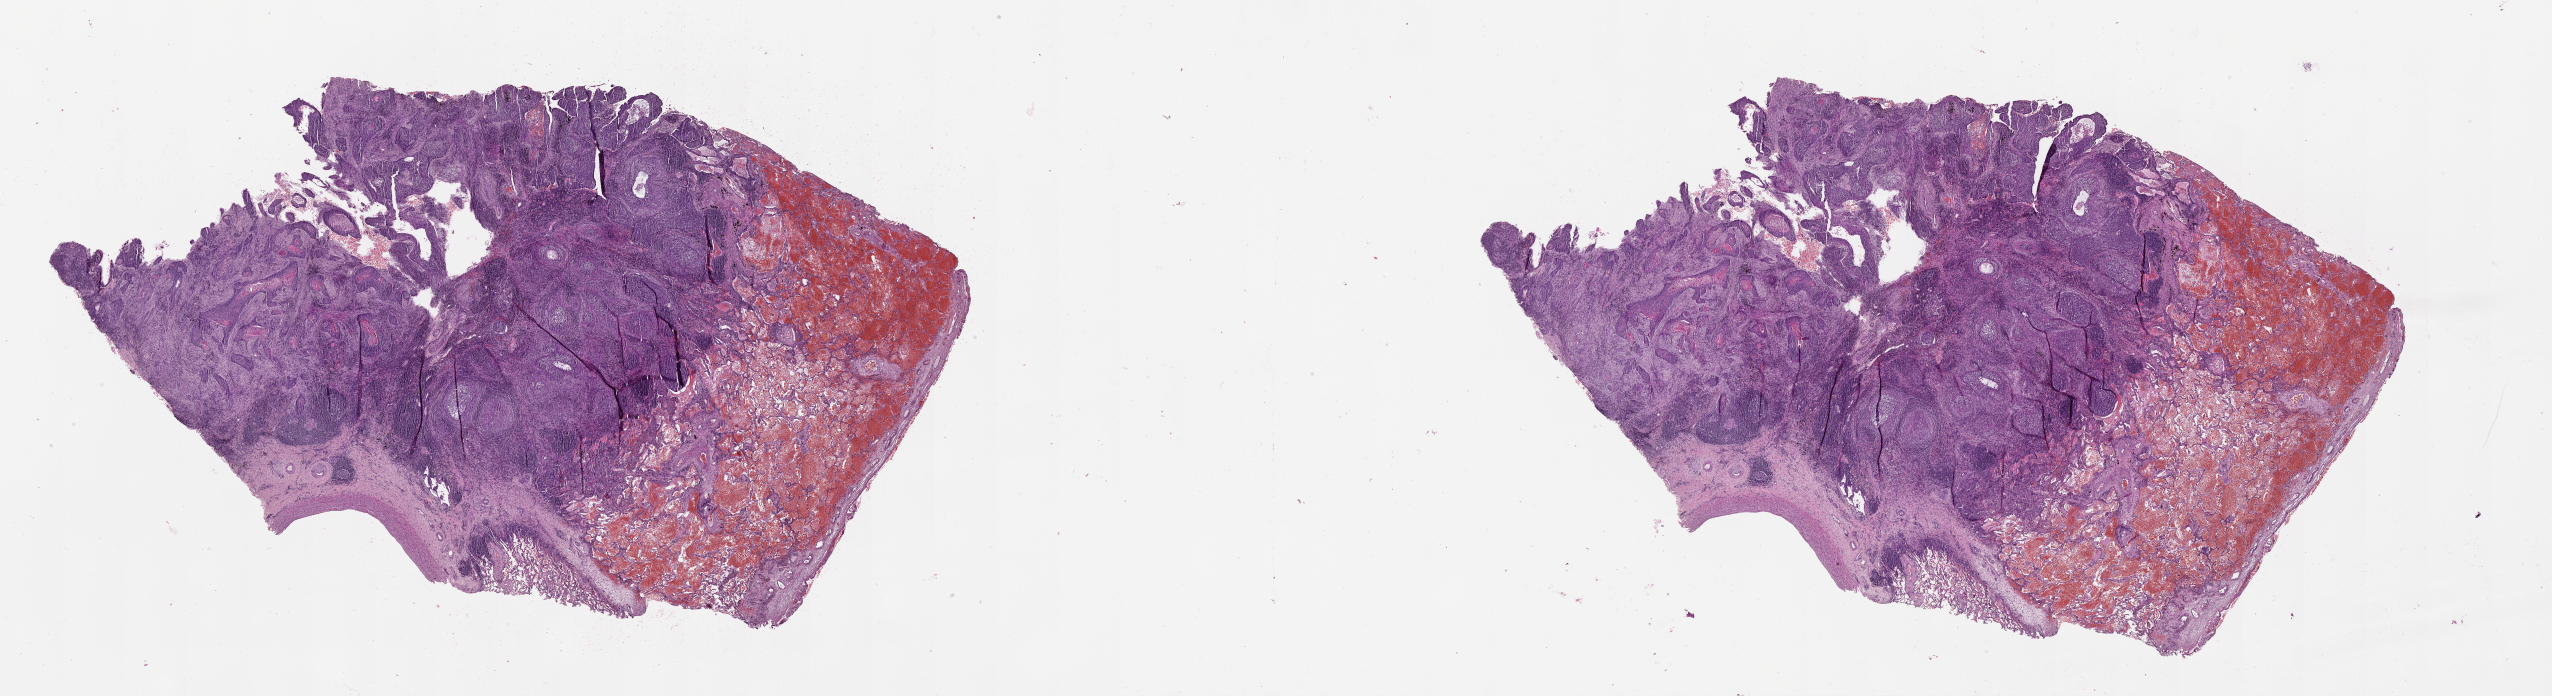
H&E whole-slide image, a low-resolution overview of the entire scanned area, about 41.1 x 11.2 mm (slide scanned at 20x), tumour tissue sample, lung. 63-year-old female patient.
• patient diagnosis (cohort enrolment): squamous cell carcinoma (lung)